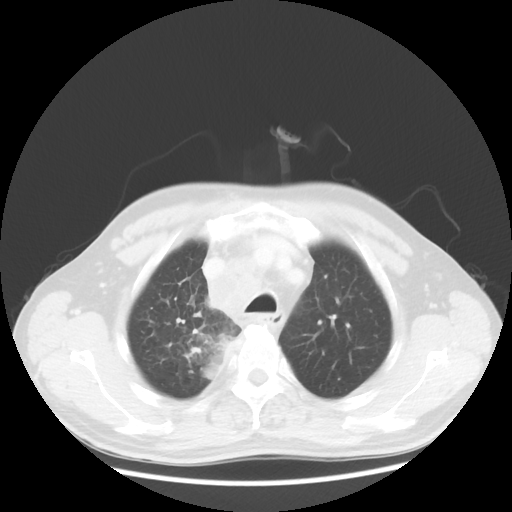
Chest CT, one axial slice; slice 98 of 124 in the series (ordered by position); reconstruction kernel STANDARD; lung window (W 1500 / L -600 HU); 512 × 512 image matrix. Patient: male, 64 years. From the clinical record (not read from this slice): clinical TNM (as recorded): T3 N3 M0; histopathological grade: G3.
Outlined on this slice (bounding box drawn by a radiologist):
- lung tumour (recorded histology: small cell carcinoma): box from (x=189, y=314) to (x=239, y=390) px